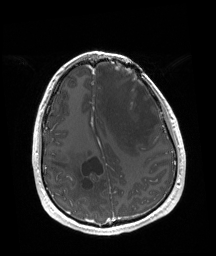
Brain MRI from a brain-tumour surgery series, one axial slice; position 57 of 192 along the scan axis; T1-weighted post-contrast; 216 × 256 image matrix, field of view 219 × 260 mm.
Outlined on this slice (manually delineated by an expert):
- tumour: bounding box <124,68,138,85> (left, top, right, bottom; pixels)